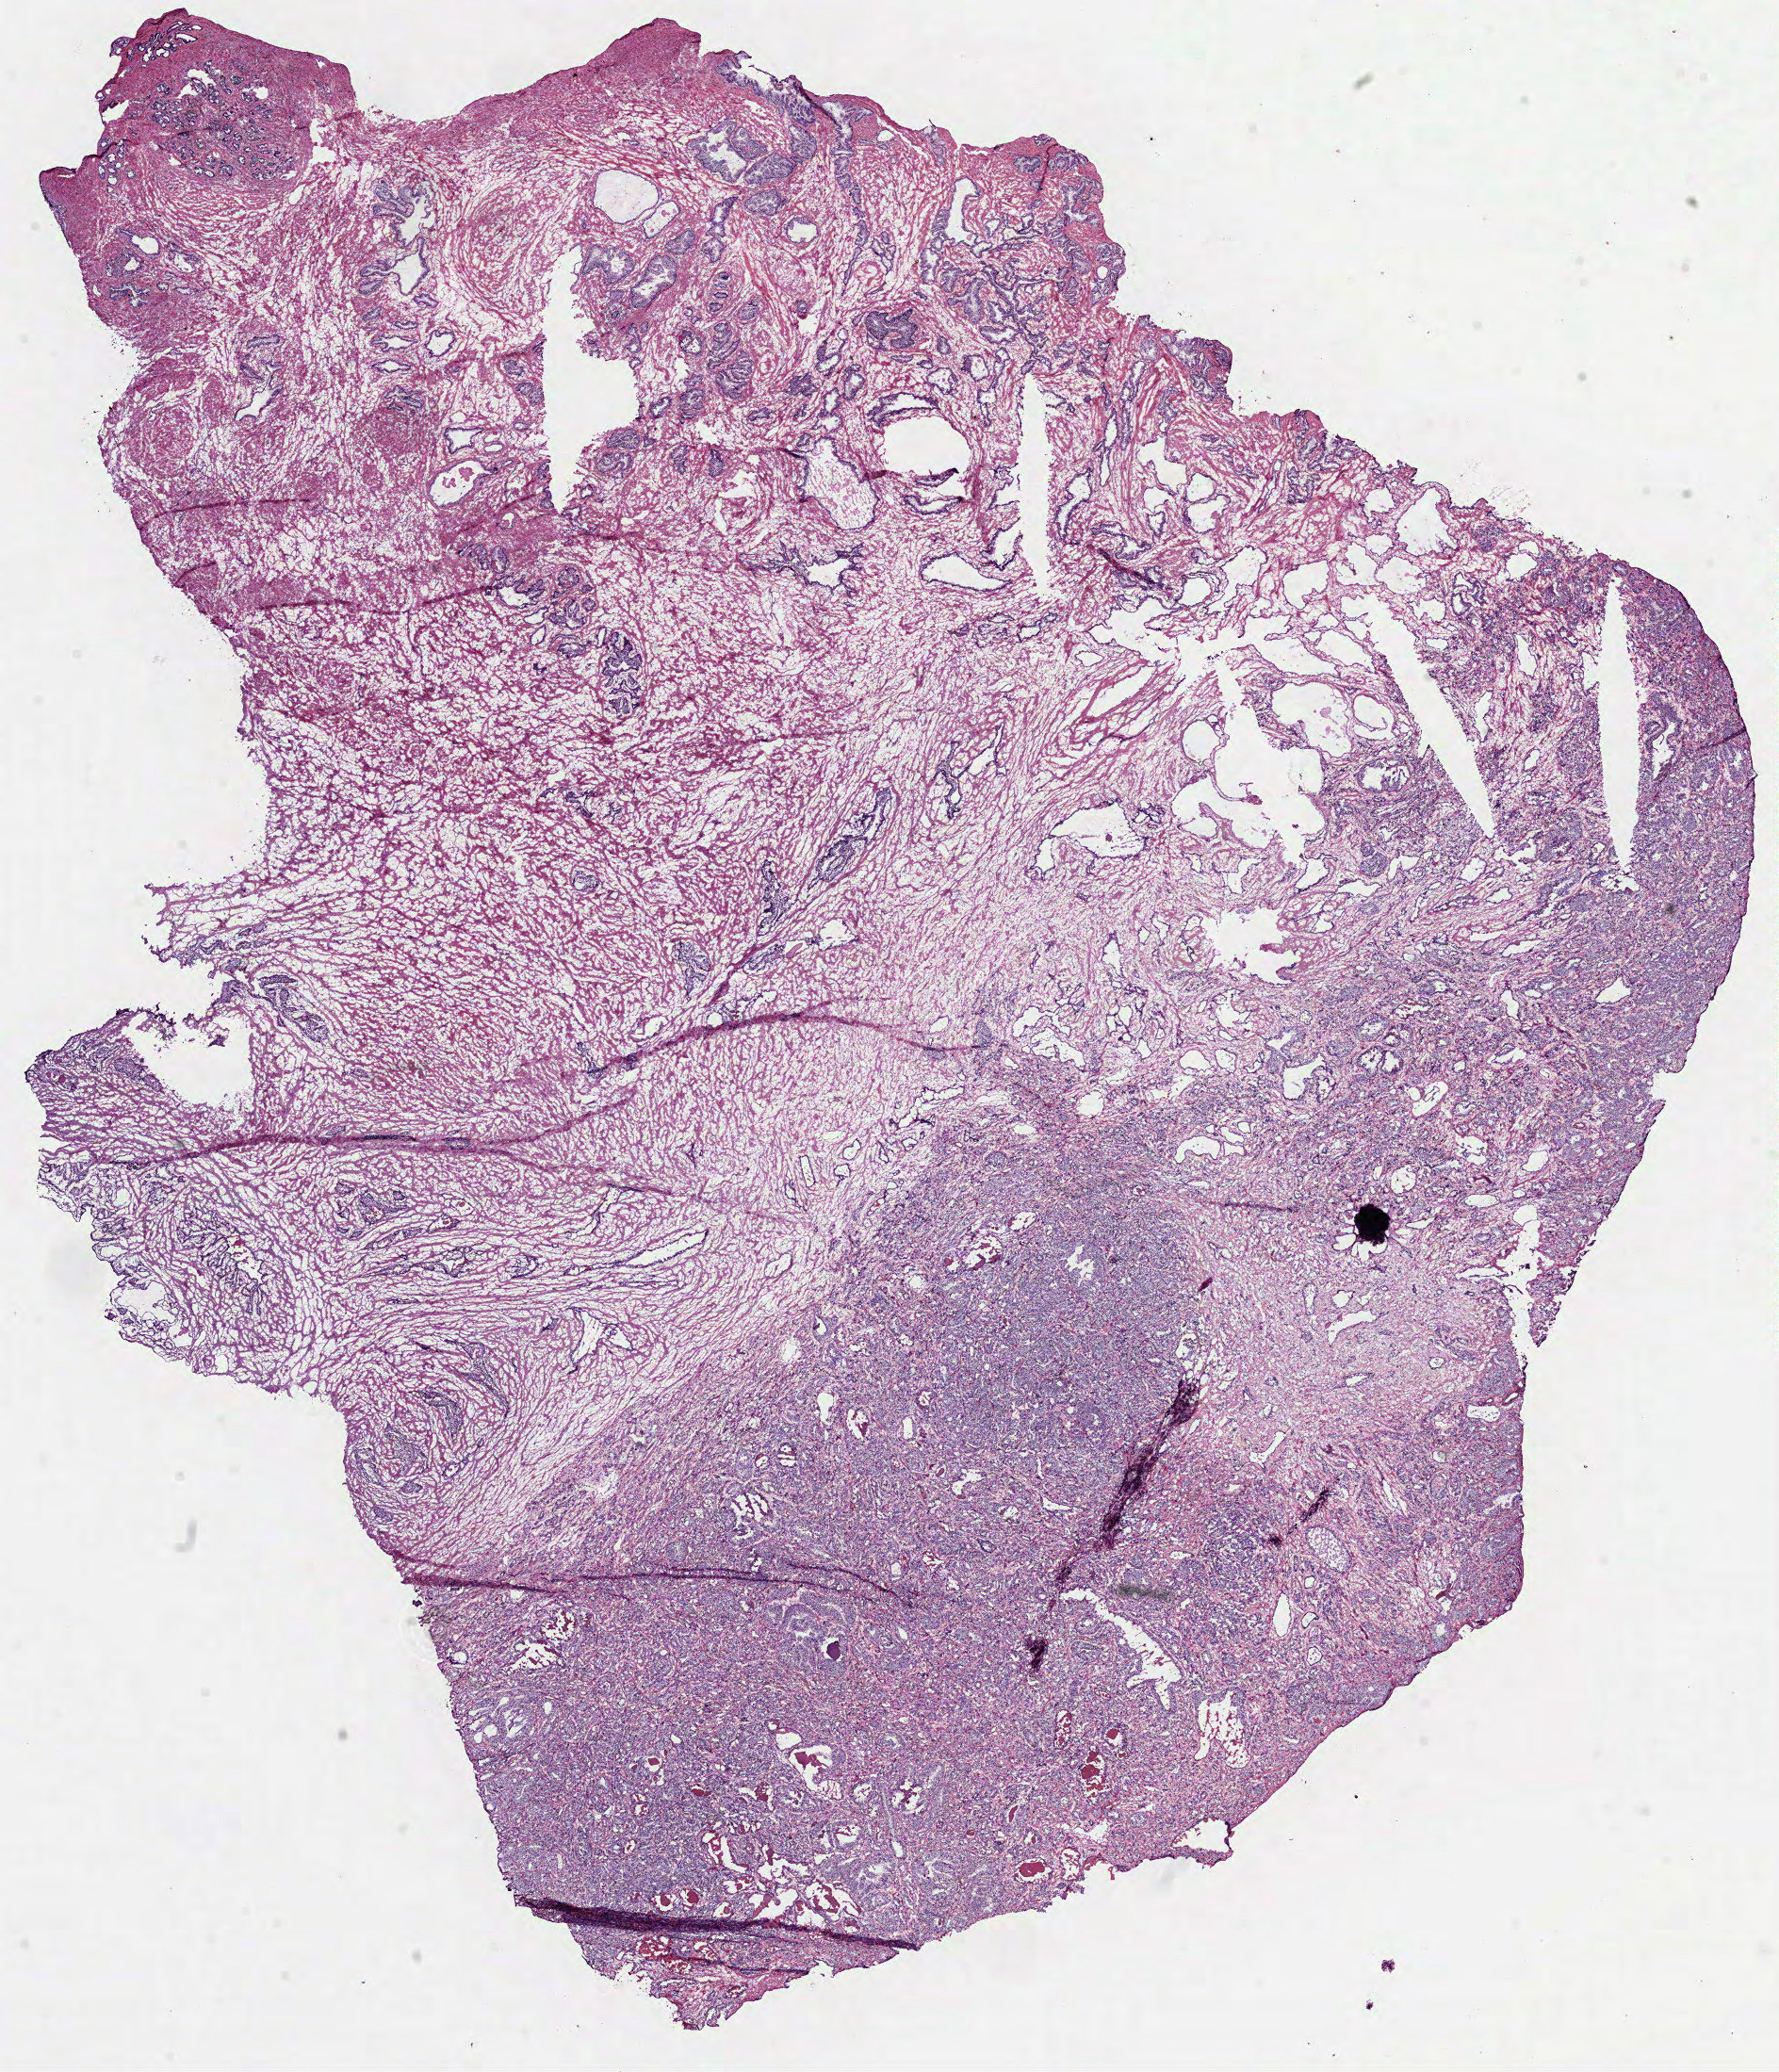
H&E whole-slide image, whole scanned area (about 15.2 x 17.7 mm, from a 40x scan) shown as a low-resolution overview; frozen section from the bottom of the tissue portion; primary tumour sample from the prostate. Patient: male, age at initial diagnosis 68 years. Gleason score: 7 (4+3). Slide review estimates, as recorded: tumour cells 60%, tumour nuclei 55%, normal cells 25%, stromal cells 15%, necrosis 0%. Infiltration values recorded for this section: lymphocyte infiltration 3%, monocyte infiltration 0%, neutrophil infiltration 0%.
* lymph nodes positive (case pathology): 0 of 18 examined
* pathologic diagnosis: Acinar cell carcinoma (prostate gland)